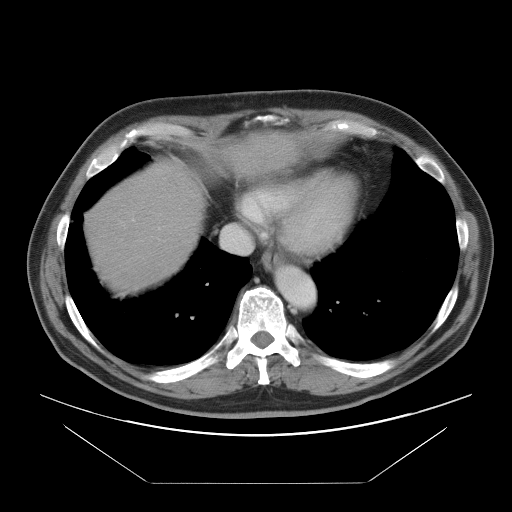
Contrast-enhanced abdominal CT, one axial slice; slice 85 of 97 in the series (ordered by position); intravenous contrast given; soft-tissue window (W 400 / L 40 HU); 5 mm slice thickness; 512 × 512 image matrix. Male patient, age 62 years. Case-level facts recorded for this patient, not image findings: diagnosis: colorectal cancer liver metastases, imaged before liver resection; multiple liver metastases: no; largest metastasis: 7 cm.
Annotated regions visible in this slice (outlined manually by an expert reader):
- hepatic veins: box from (x=221, y=199) to (x=264, y=255) px
- liver: (x=88, y=136)–(x=292, y=291)
- planned liver remnant (the part of the liver to remain after resection): (x=88, y=183)–(x=201, y=293)